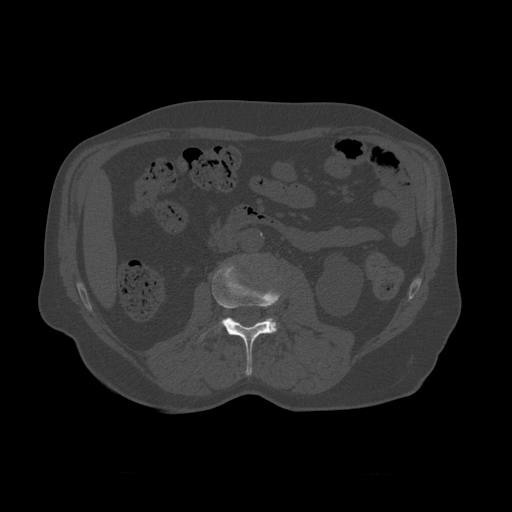
CT including the spine, one axial slice. Slice 325 of 450 in the series (ordered by position). Reconstruction kernel STANDARD. 120 kVp. Bone window (W 1800 / L 400 HU). 512 × 512 image matrix, field of view 405 × 405 mm. Patient age 75 years. Case-level facts recorded for this patient, not image findings: primary cancer: prostate.
Outlined on this slice (semi-automatically segmented with operator editing):
- L2 vertebra: box from (x=200, y=263) to (x=281, y=376) px
- L3 vertebra: (x=269, y=318)–(x=279, y=333)